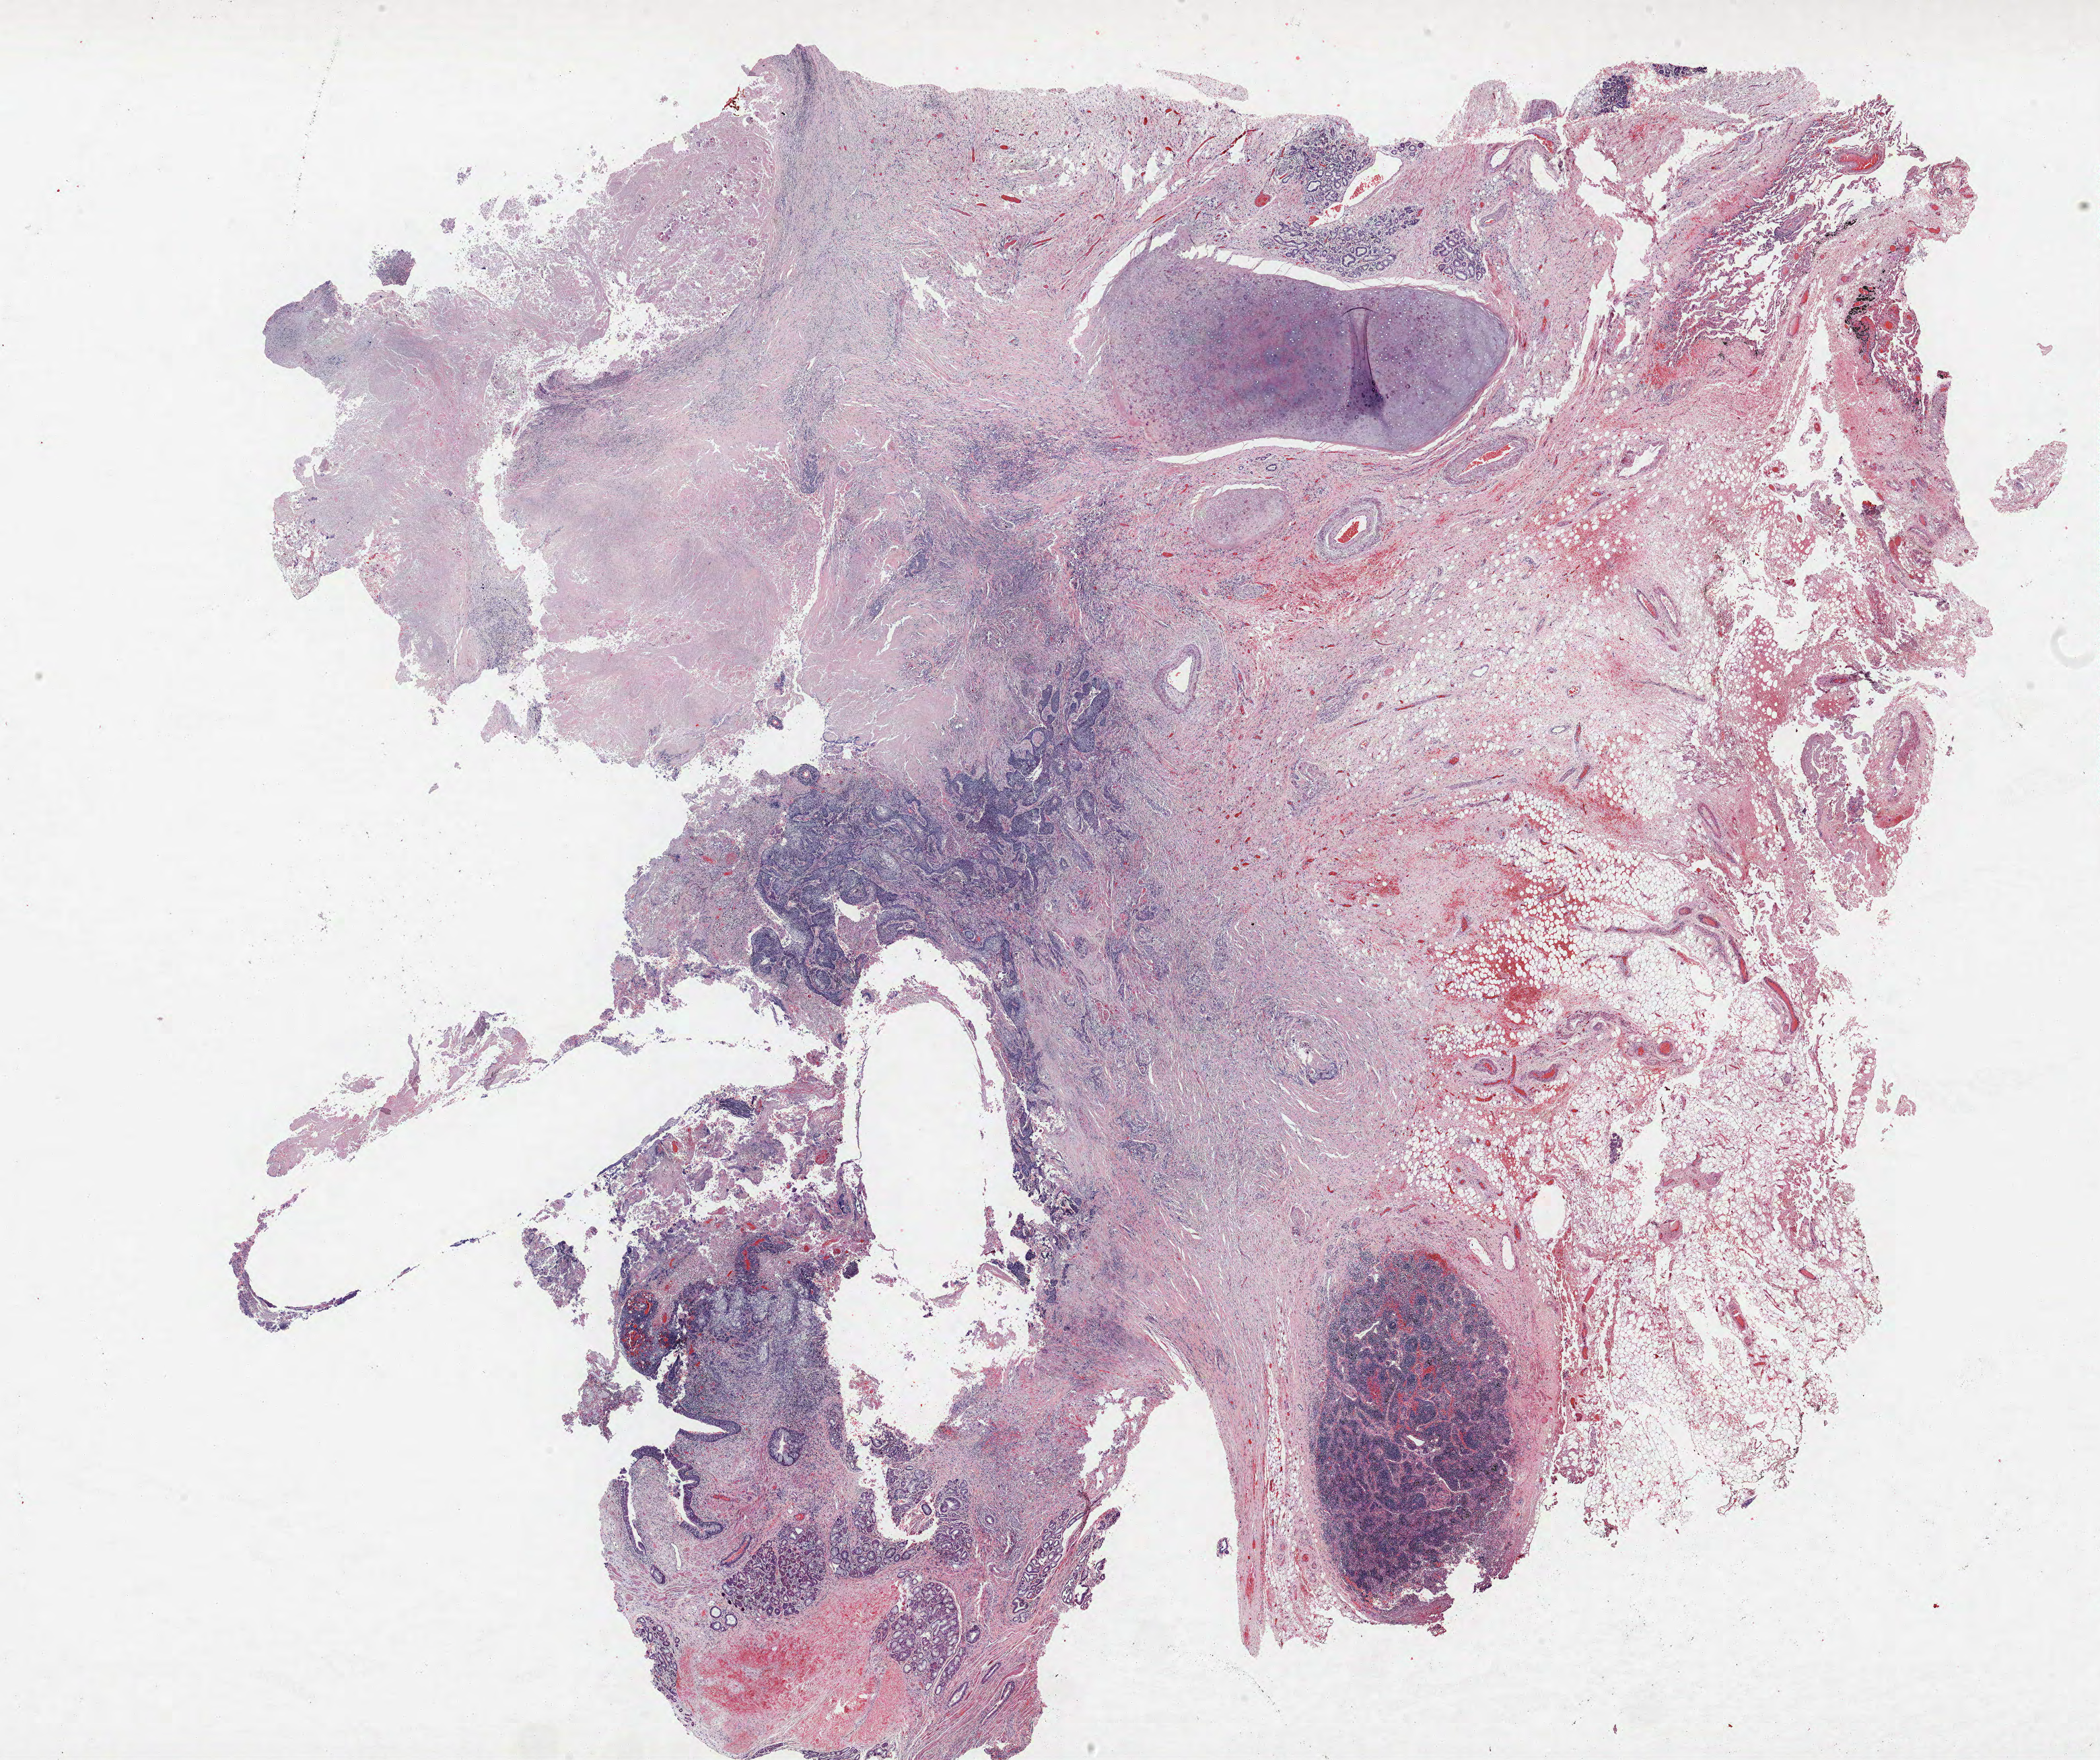
H&E-stained whole-slide image — shown as a low-resolution overview of the whole scanned area (about 25.0 x 20.9 mm), formalin-fixed paraffin-embedded (FFPE) section, lung. Male patient, aged 62 at enrolment. Current smoker at enrolment.
Participant's lung-cancer diagnosis: Squamous cell carcinoma, NOS (ICD-O-3 8070/3).